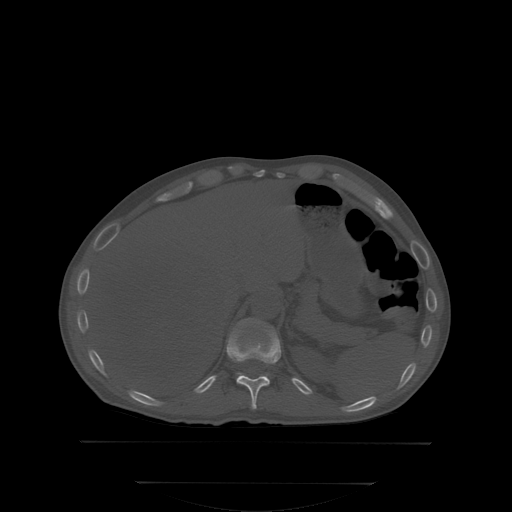
CT including the spine, one axial slice; bone window (W 1800 / L 400 HU); 512 × 512 image matrix, field of view 500 × 500 mm. Male patient, age 58 years. From the clinical record (not read from this slice): primary cancer: prostate.
Structures marked on this image (semi-automatic segmentation, software-assisted and operator-edited):
- T11 vertebra: box from (x=228, y=332) to (x=280, y=408) px
- T12 vertebra: (x=231, y=318)–(x=274, y=374)